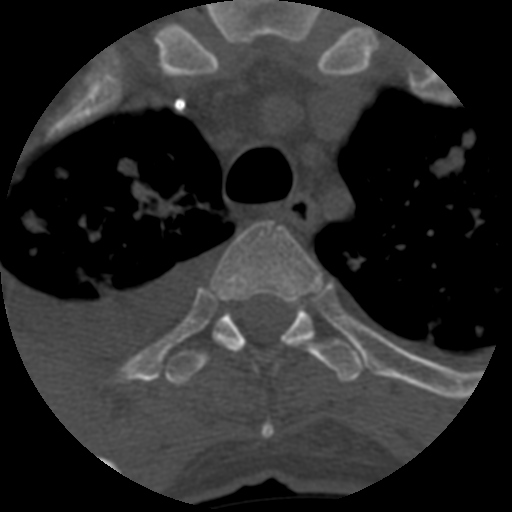
CT including the spine, one axial slice. Slice 480 of 708 in the series (ordered by position). Reconstruction kernel STANDARD. 120 kVp. One of 3 acquisitions stored at this slice position. Bone window (W 1800 / L 400 HU). 1.25 mm slice thickness. 512 × 512 image matrix, field of view 160 × 160 mm. Patient age 55 years. From the clinical record (not read from this slice): primary cancer: colon; vertebrae with lytic lesions (as recorded): T12, L1, L5.
Outlined on this slice (semi-automatic segmentation, software-assisted and operator-edited):
- T3 vertebra: box from (x=215, y=221) to (x=322, y=439) px
- T4 vertebra: (x=164, y=295)–(x=365, y=387)